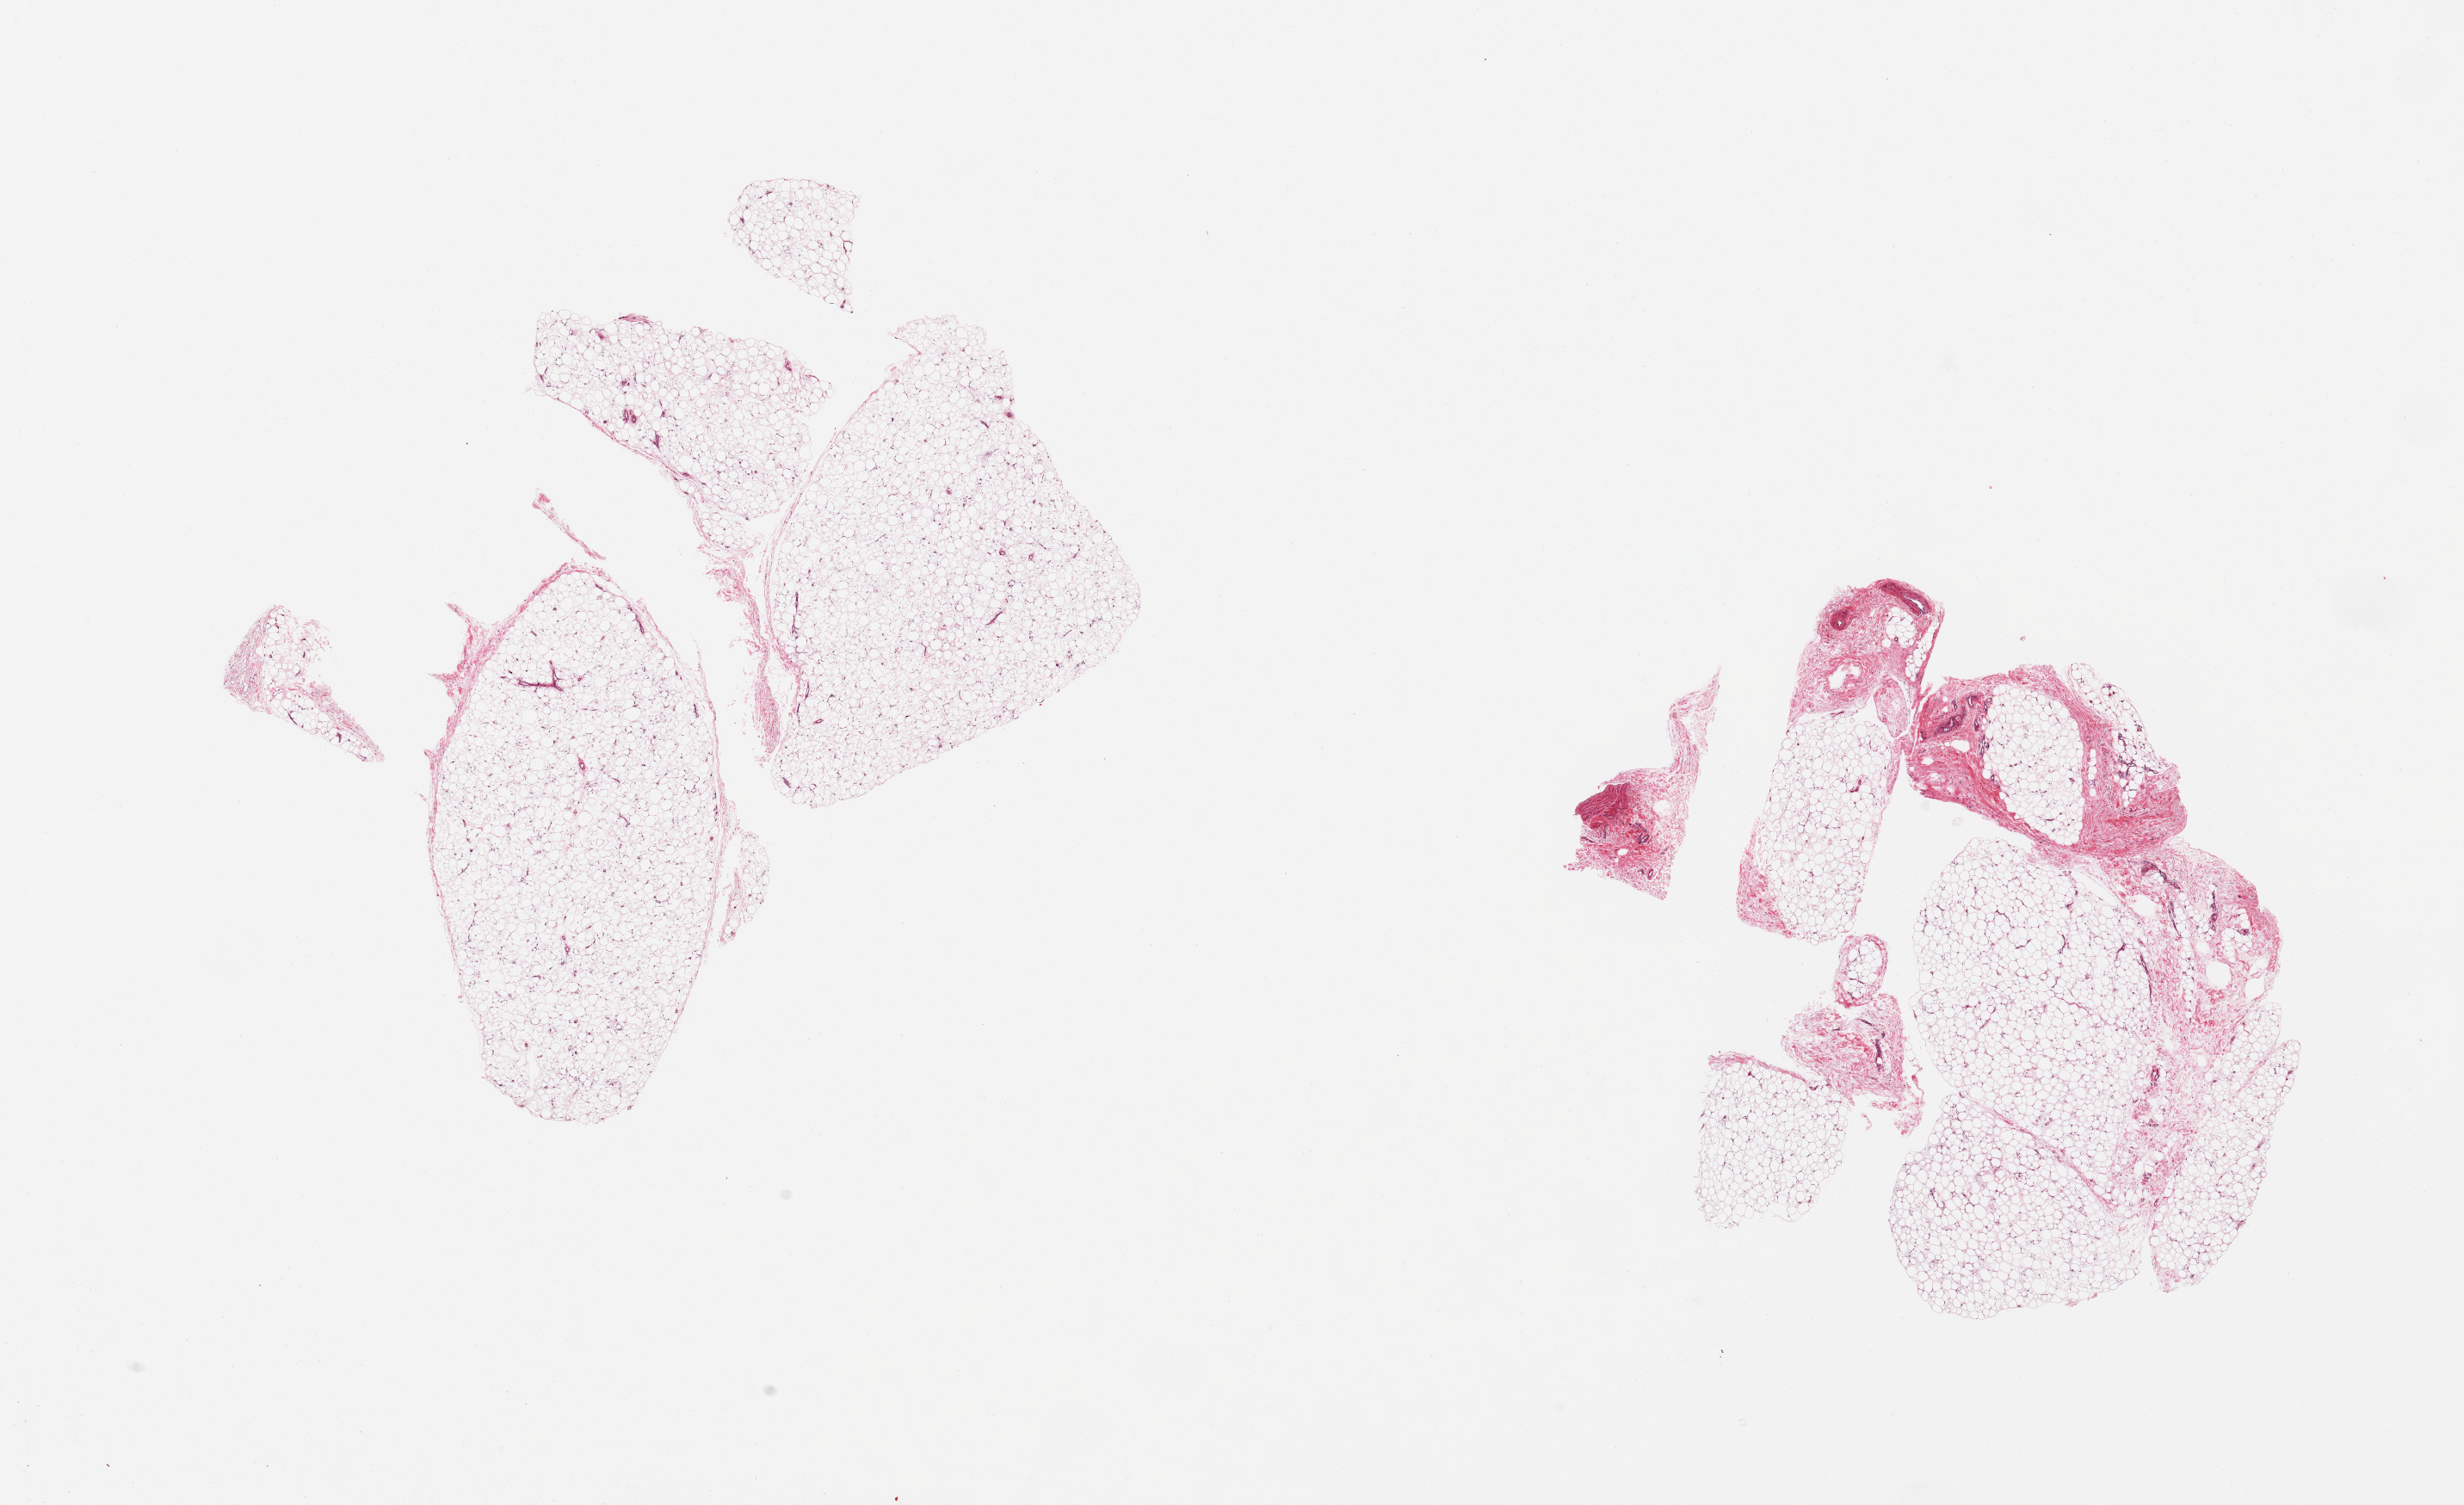
Haematoxylin and eosin whole-slide image, brightfield — low-resolution overview of the scanned area, about 22.6 x 13.8 mm. PAXgene-fixed paraffin-embedded (PFPE) section. Section of adipose tissue (target tissue). Tissue donor sample.
Pathologist's review note for this sample: 2 pieces; 1 pure fat, 1 has 20% fibrous tissue.